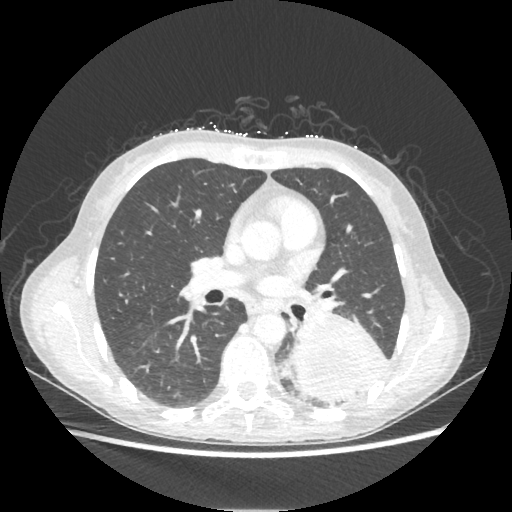
Chest CT, one axial slice. Position 120 of 221 along the scan axis. Reconstruction kernel STANDARD. Lung window (W 1500 / L -600 HU). 1.25 mm slice thickness. 512 × 512 image matrix. Patient: female, 53 years. Case-level facts recorded for this patient, not image findings: clinical TNM (as recorded): T3 N0 M0.
Outlined on this slice (rectangle marked by the reading radiologist):
- lung tumour (recorded histology: adenocarcinoma): bounding box <288,311,390,403> (left, top, right, bottom; pixels)